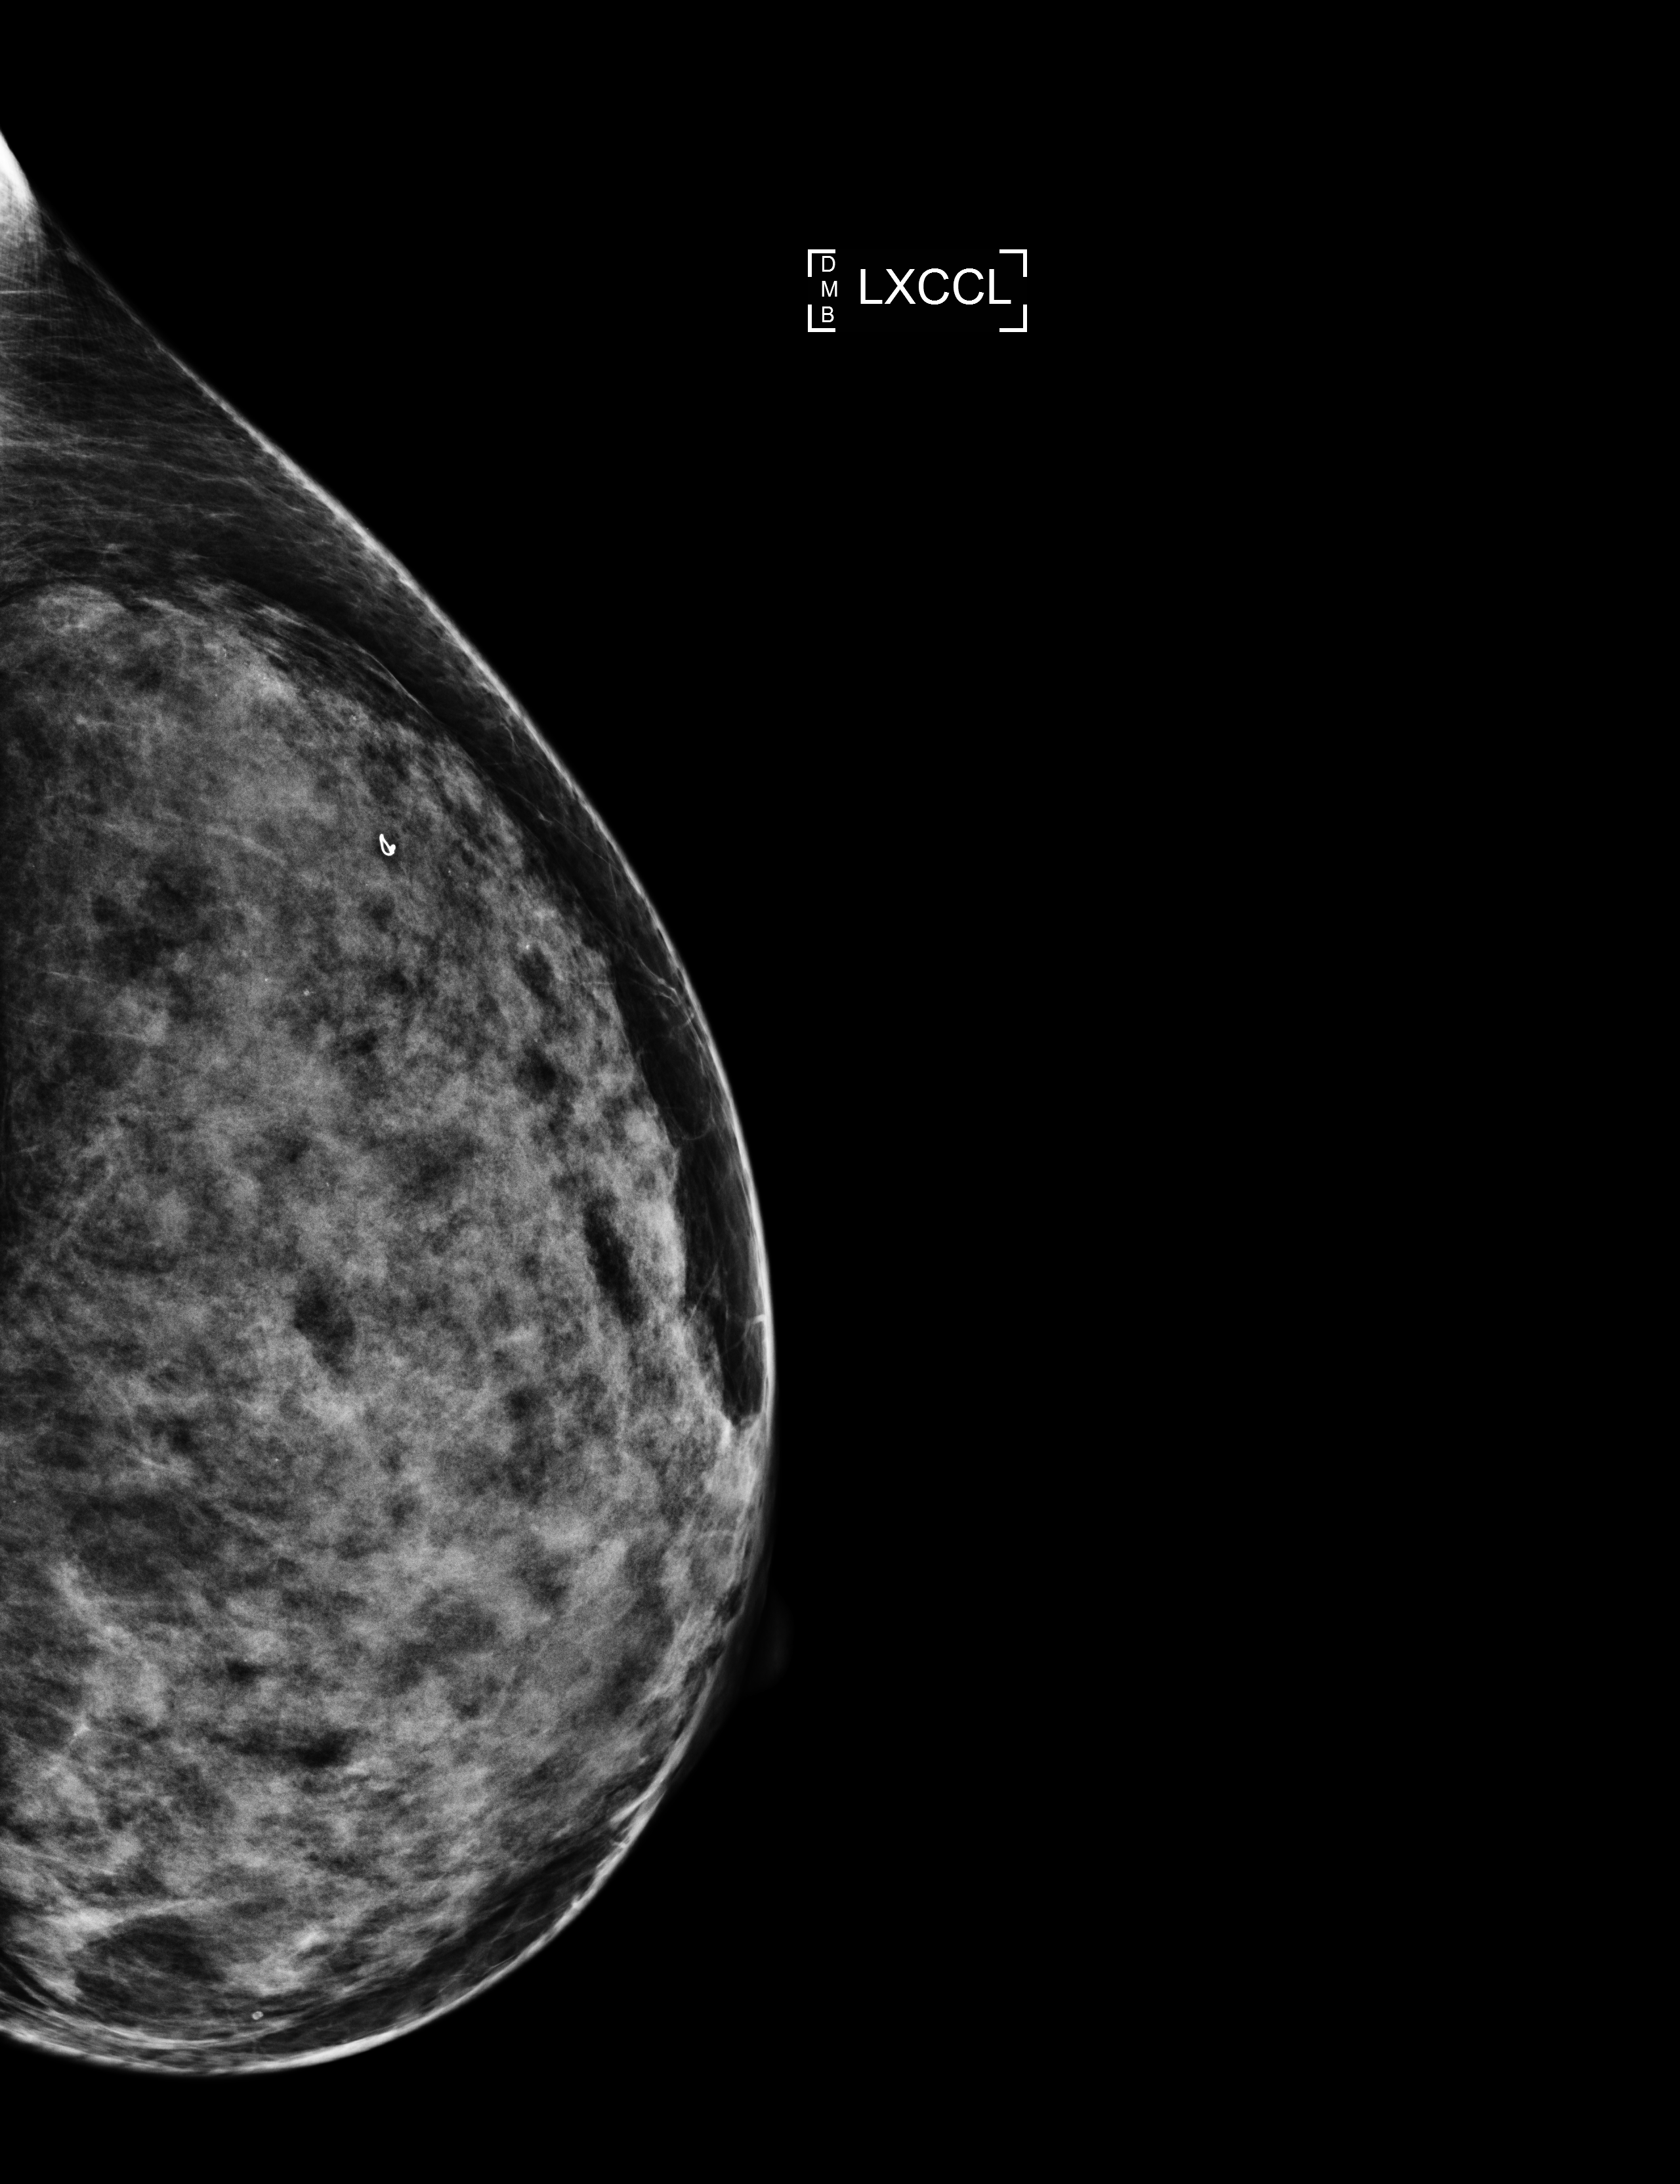
Full-field digital mammogram (FFDM), left breast, laterally exaggerated craniocaudal (XCCL) view, screening examination, compressed breast thickness 62 mm, system: Selenia Dimensions. Female patient, age 62 years.
Breast density at the screening exam (both breasts): extremely dense (BI-RADS density category d). Final BI-RADS category for the screening round (tomosynthesis exam, both breasts): category 1. Recall: no recall after this screen.